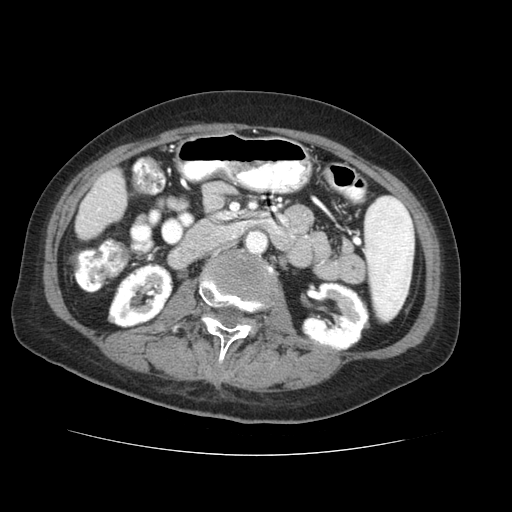
Contrast-enhanced abdominal CT (liver protocol), one axial slice; slice 7 of 73 in the series (ordered by position); reconstruction kernel STANDARD; 120 kVp; soft-tissue window (W 400 / L 40 HU); 2.5 mm slice thickness; 512 × 512 image matrix, field of view 360 × 360 mm. Case-level facts recorded for this patient, not image findings: diagnosis: hepatocellular carcinoma (patient treated with transarterial chemoembolisation; whether this scan precedes or follows treatment is not stated here); TNM stage (as recorded): Stage-IVB; Child-Pugh class: A.
Outlined on this slice (semi-automatic segmentation, software-assisted and operator-edited):
- liver parenchyma outside the tumour (the mass and vessels are separate outlines, so this box may not span the whole liver): bounding box [x1, y1, x2, y2] px = [76, 170, 126, 240]
- liver vessels: [81, 185, 120, 225]